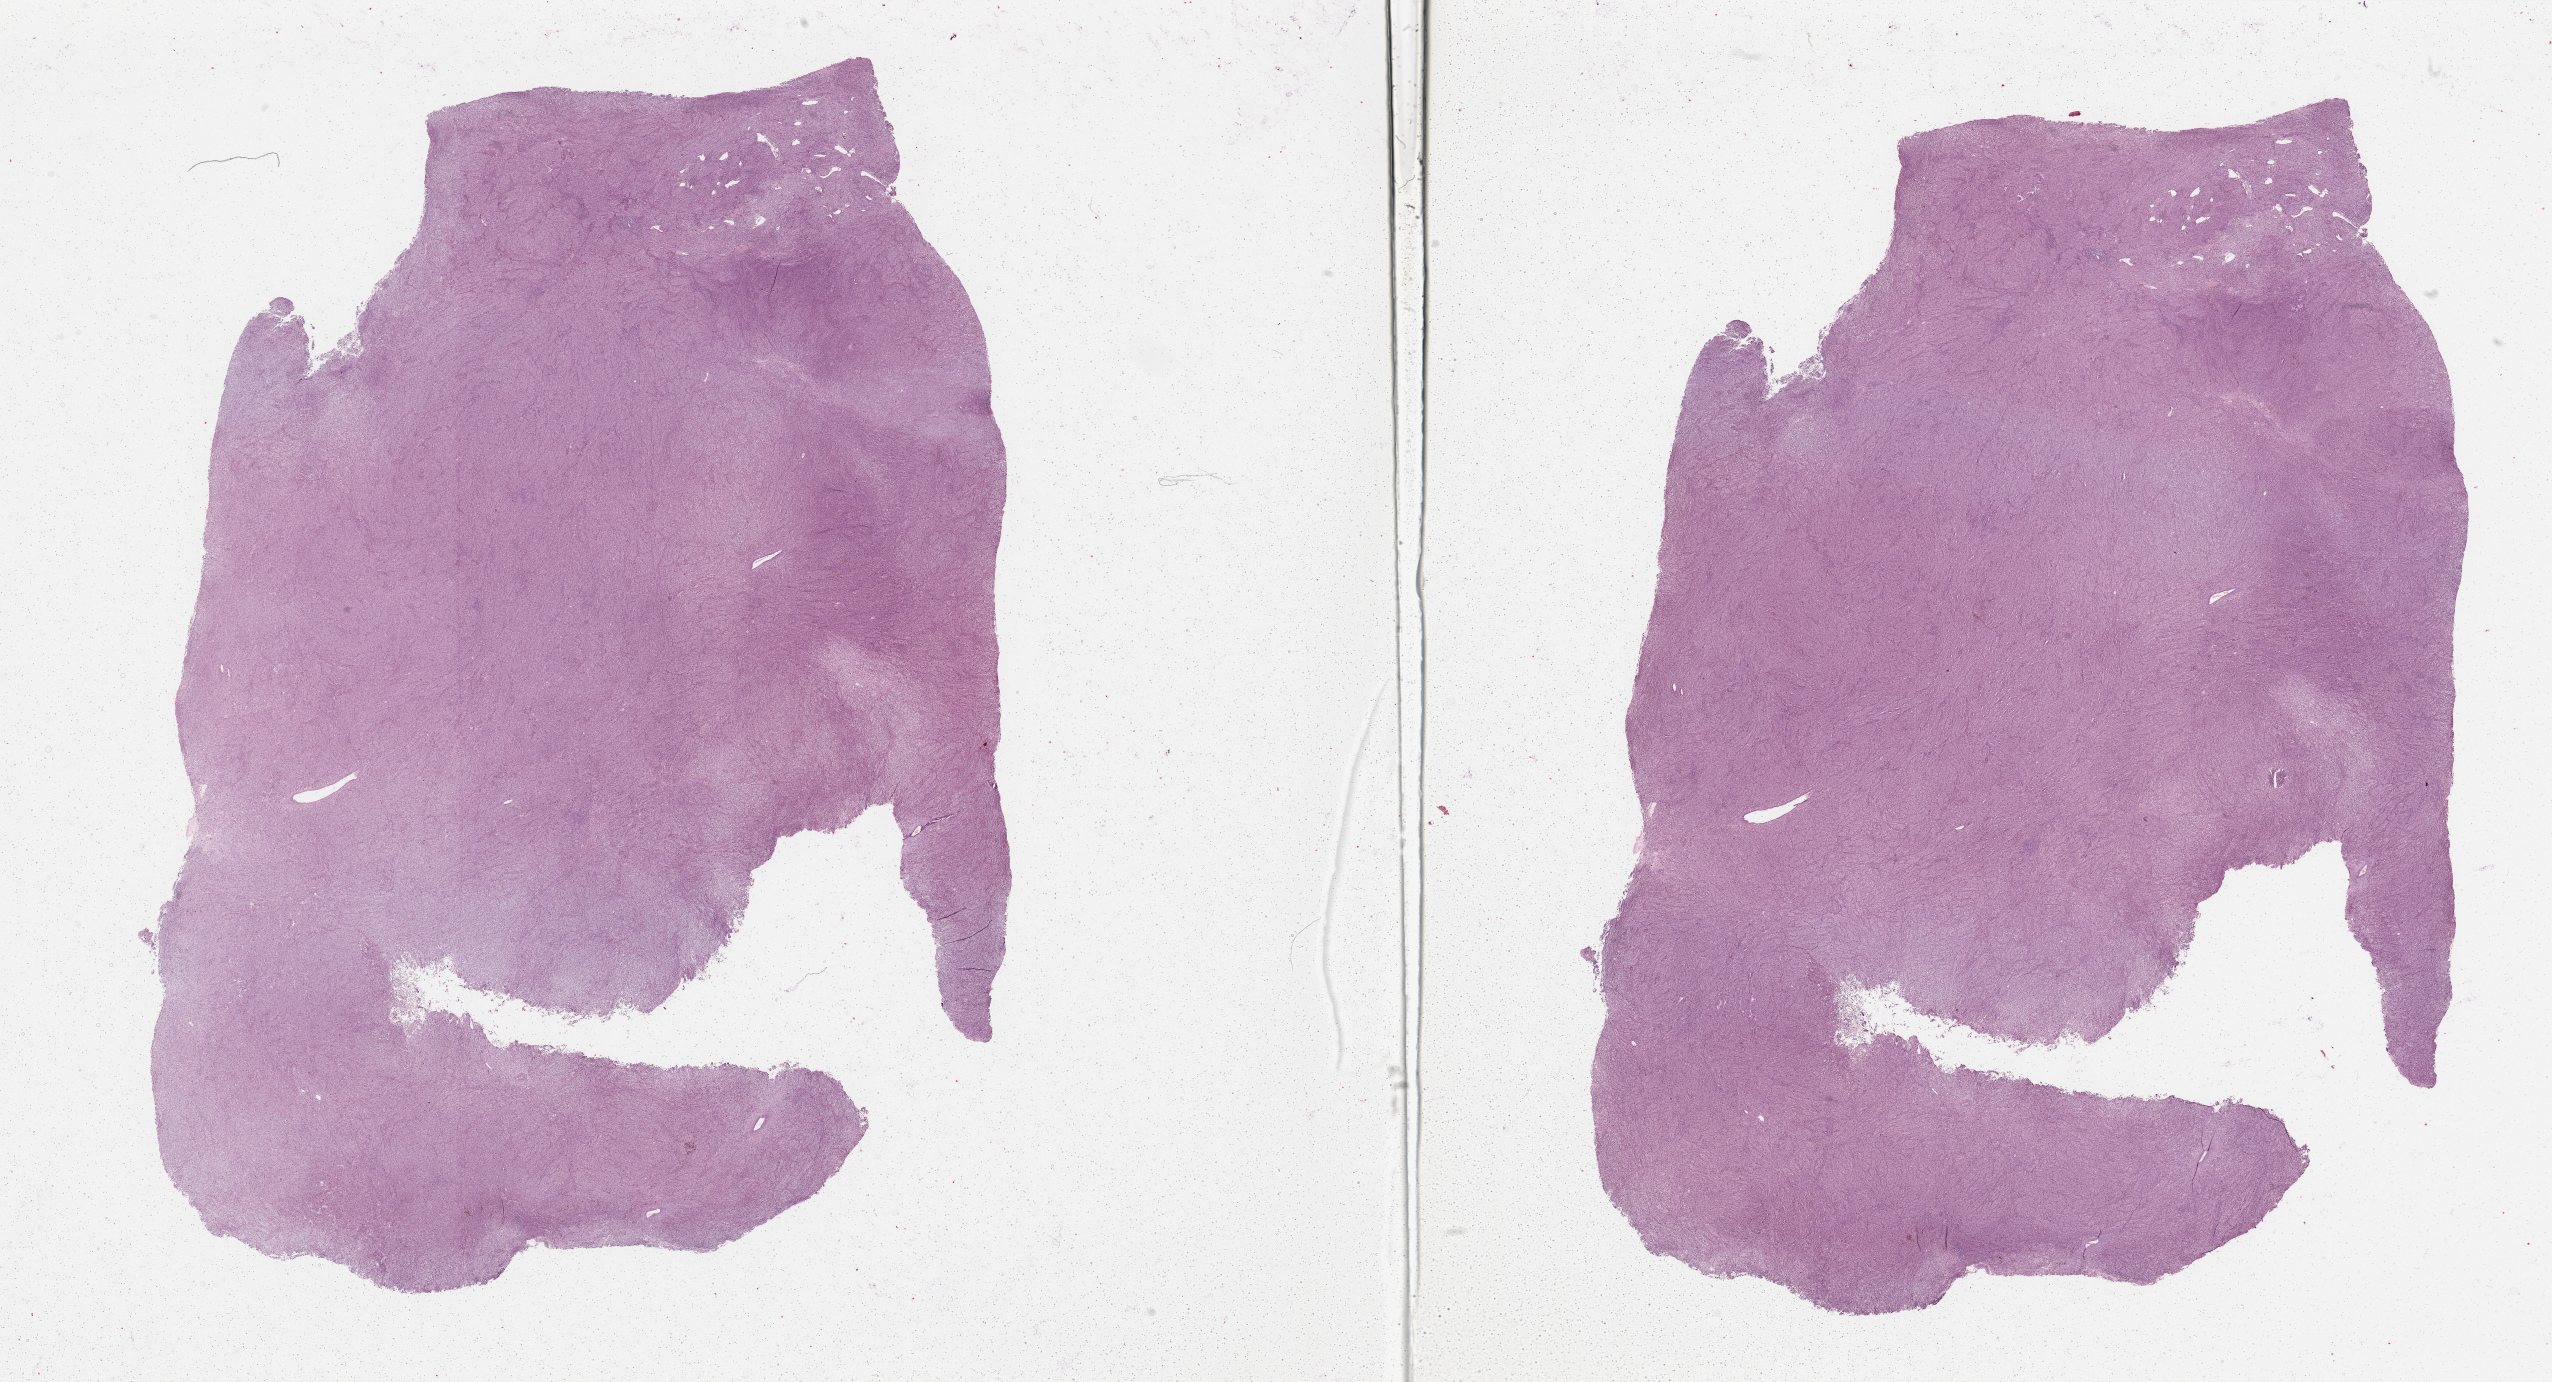
Whole-slide histology image, Hematoxylin and eosin (H&E) stained, a low-resolution overview of the entire scanned area, about 40.4 x 21.9 mm (slide scanned at 20x). Tumour tissue sample, sampled site: shoulder. Patient: male, age 74 years. Slide review estimates, as recorded: tumour nuclei 90%, necrosis 0%.
* AJCC pathologic stage: IIC
* diagnosis: Malignant melanoma, NOS